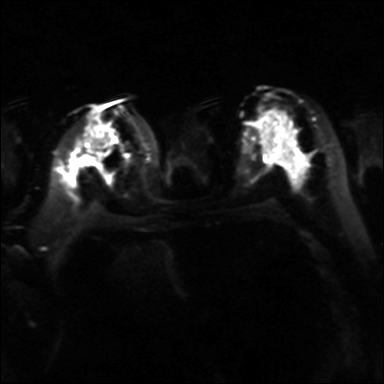
Breast MRI, one axial slice. Position 18 of 36 along the scan axis. Diffusion-weighted series; image 2 of 4 stored at this slice position (different b-values; order by instance number). 3 T. 4 mm slice thickness. 384 × 384 image matrix, field of view 320 × 320 mm. Female patient.
Structures marked on this image (manually delineated by an expert):
- tumour on diffusion-weighted imaging: bounding box (x1, y1, x2, y2) in pixels: (79, 156, 94, 165)